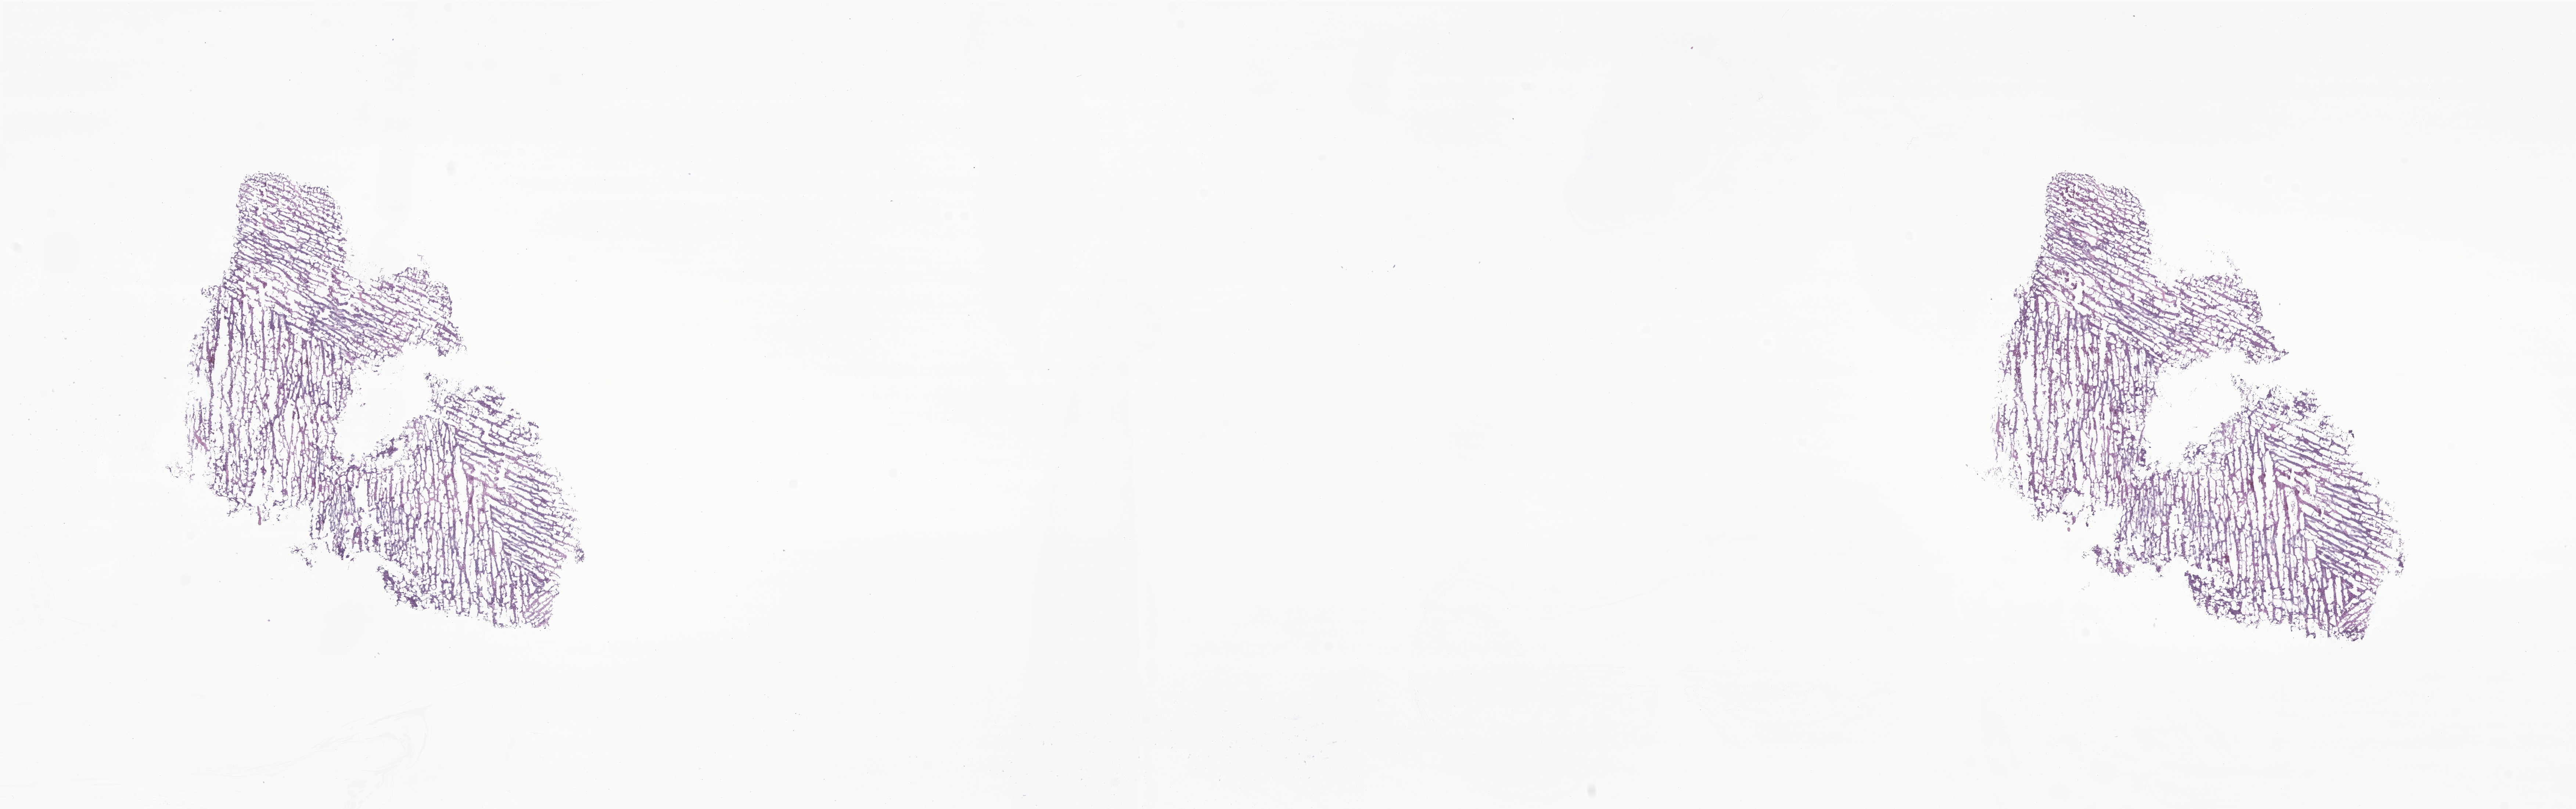
Whole-slide image, haematoxylin and eosin stain of tumor tissue from the brain stem — low-resolution overview of the scanned area, about 29.6 x 9.3 mm. Frozen section (OCT-embedded). Patient male; age 45 months (3 years 9 months).
• diagnosis (ICD-O-3 morphology term): Medulloblastoma, NOS